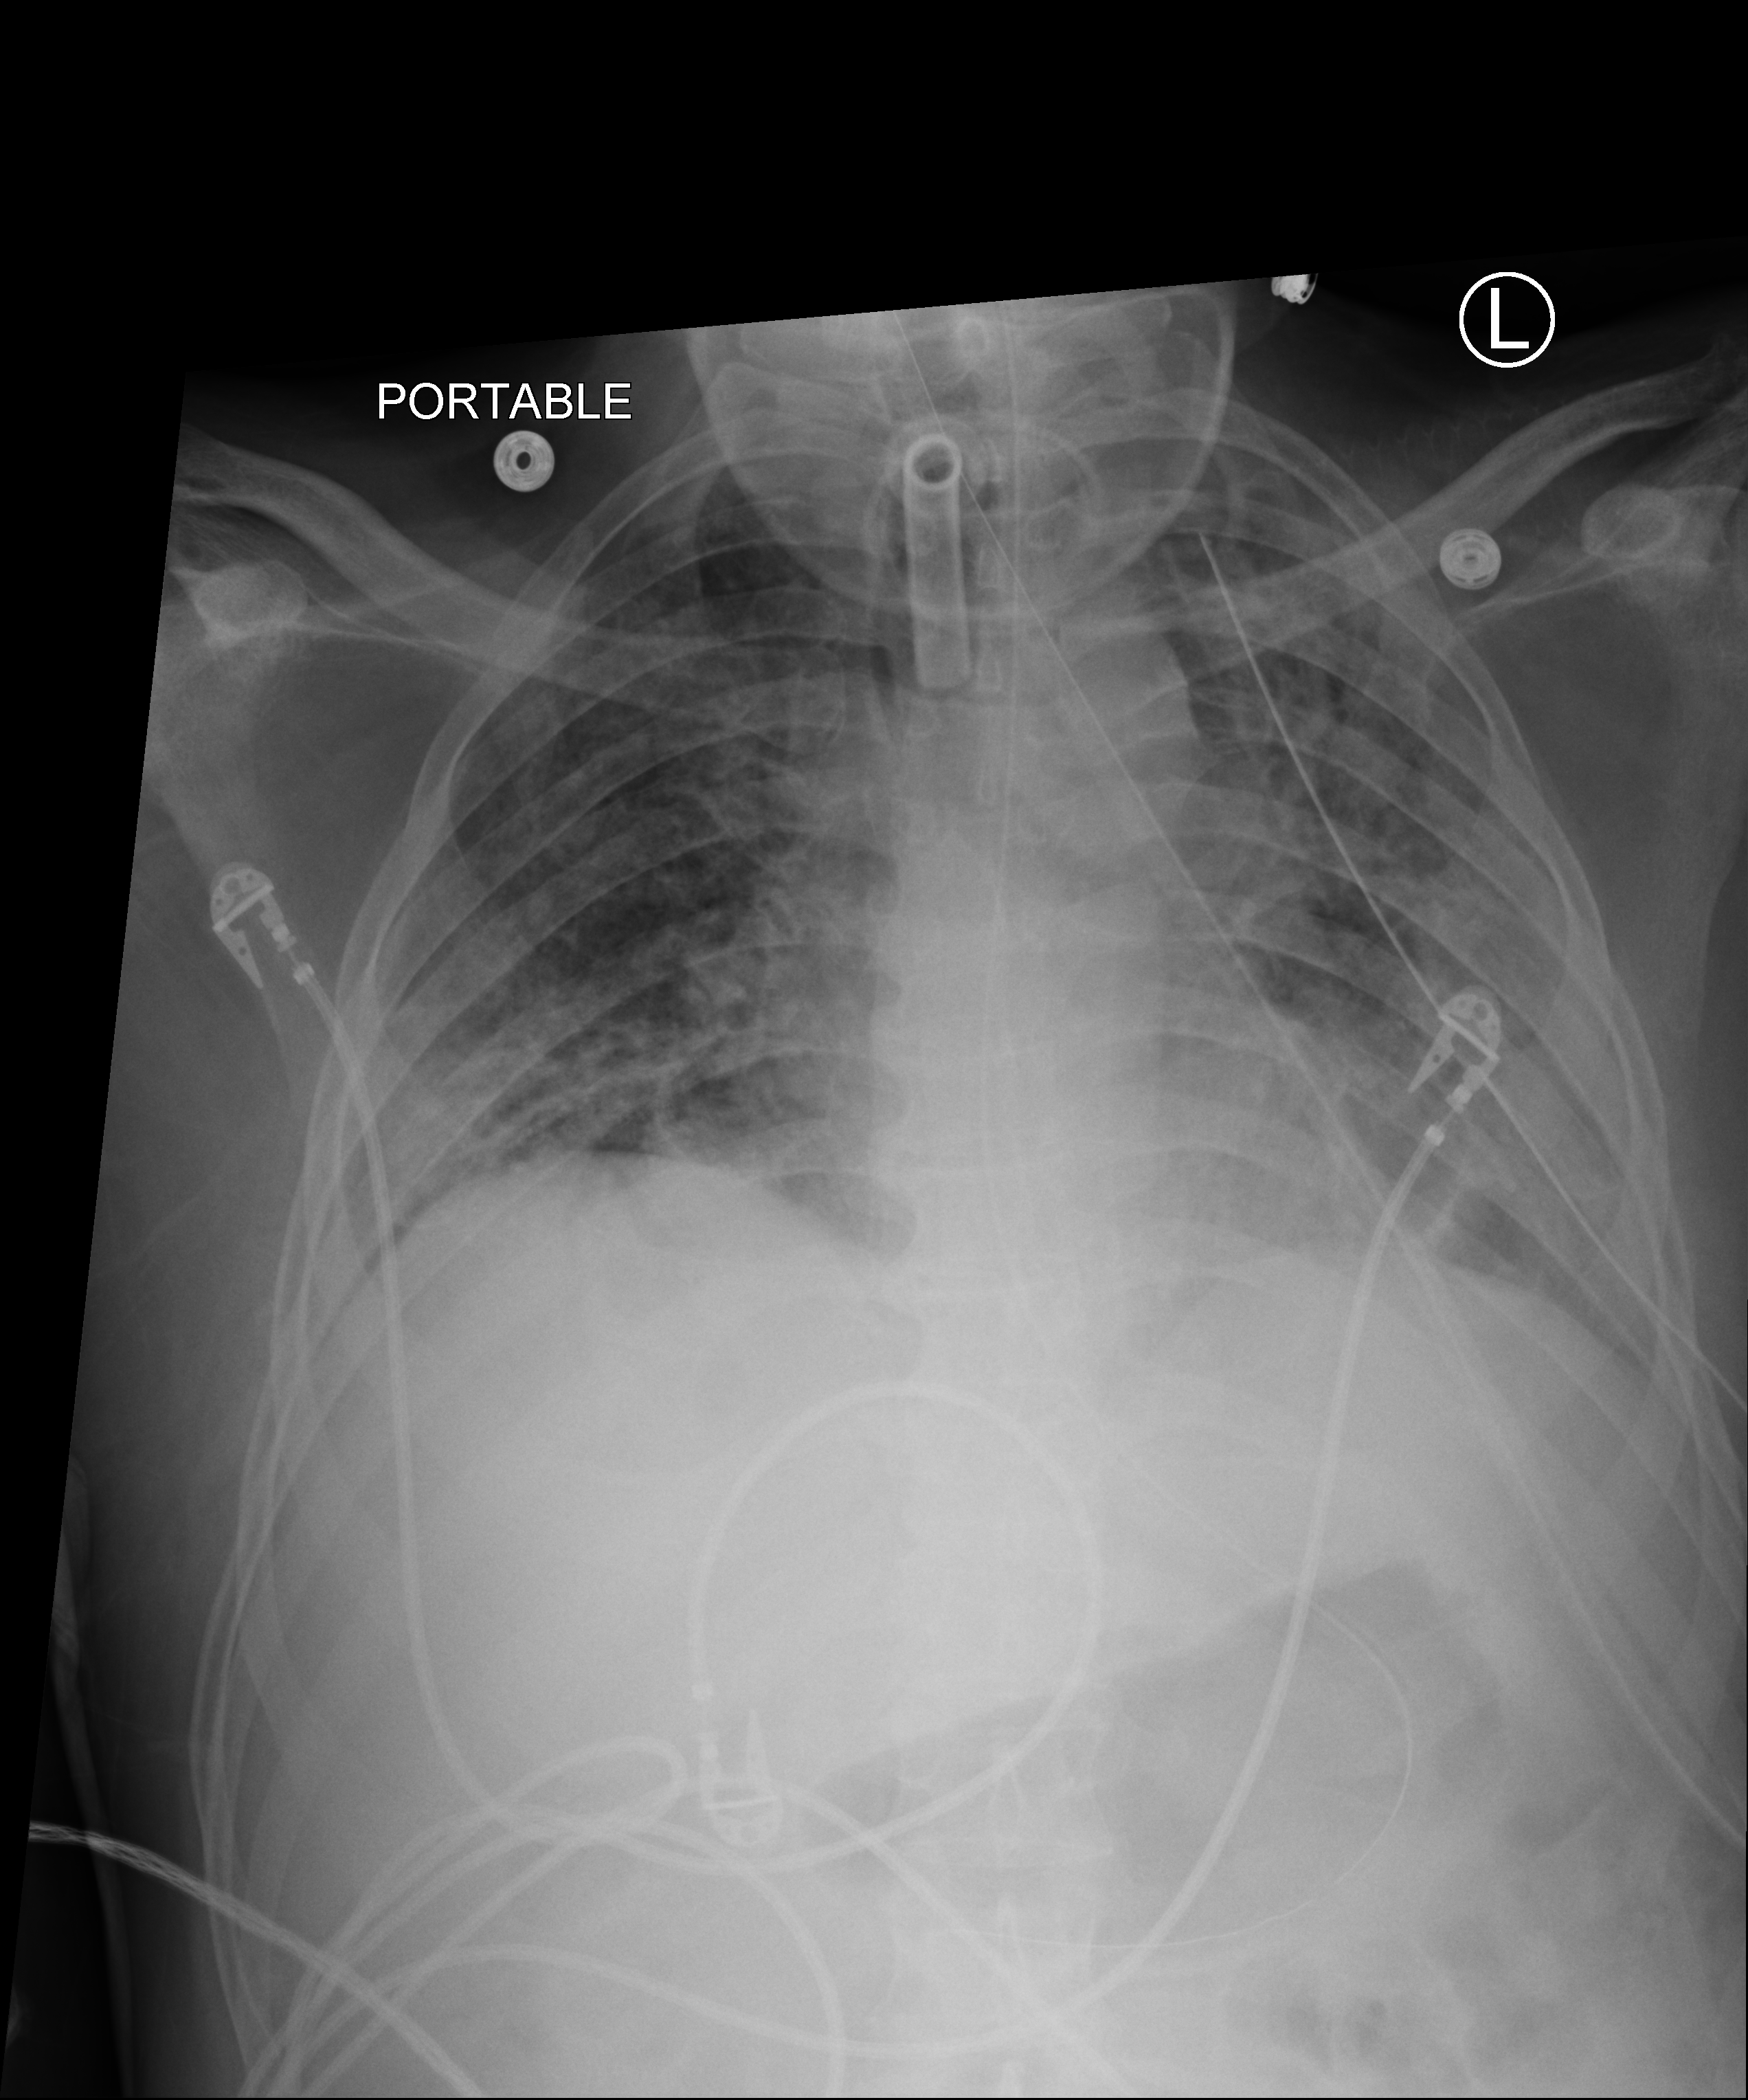
Portable chest radiograph, anteroposterior (AP) projection. Male patient hospitalised with COVID-19, age 18–59 years.
From the hospital-stay record, not from the radiograph (when in the stay this image was taken is not recorded): mechanically ventilated during this hospital stay: yes; length of hospital stay: 83 days; admitted to intensive care during this hospital stay: yes.